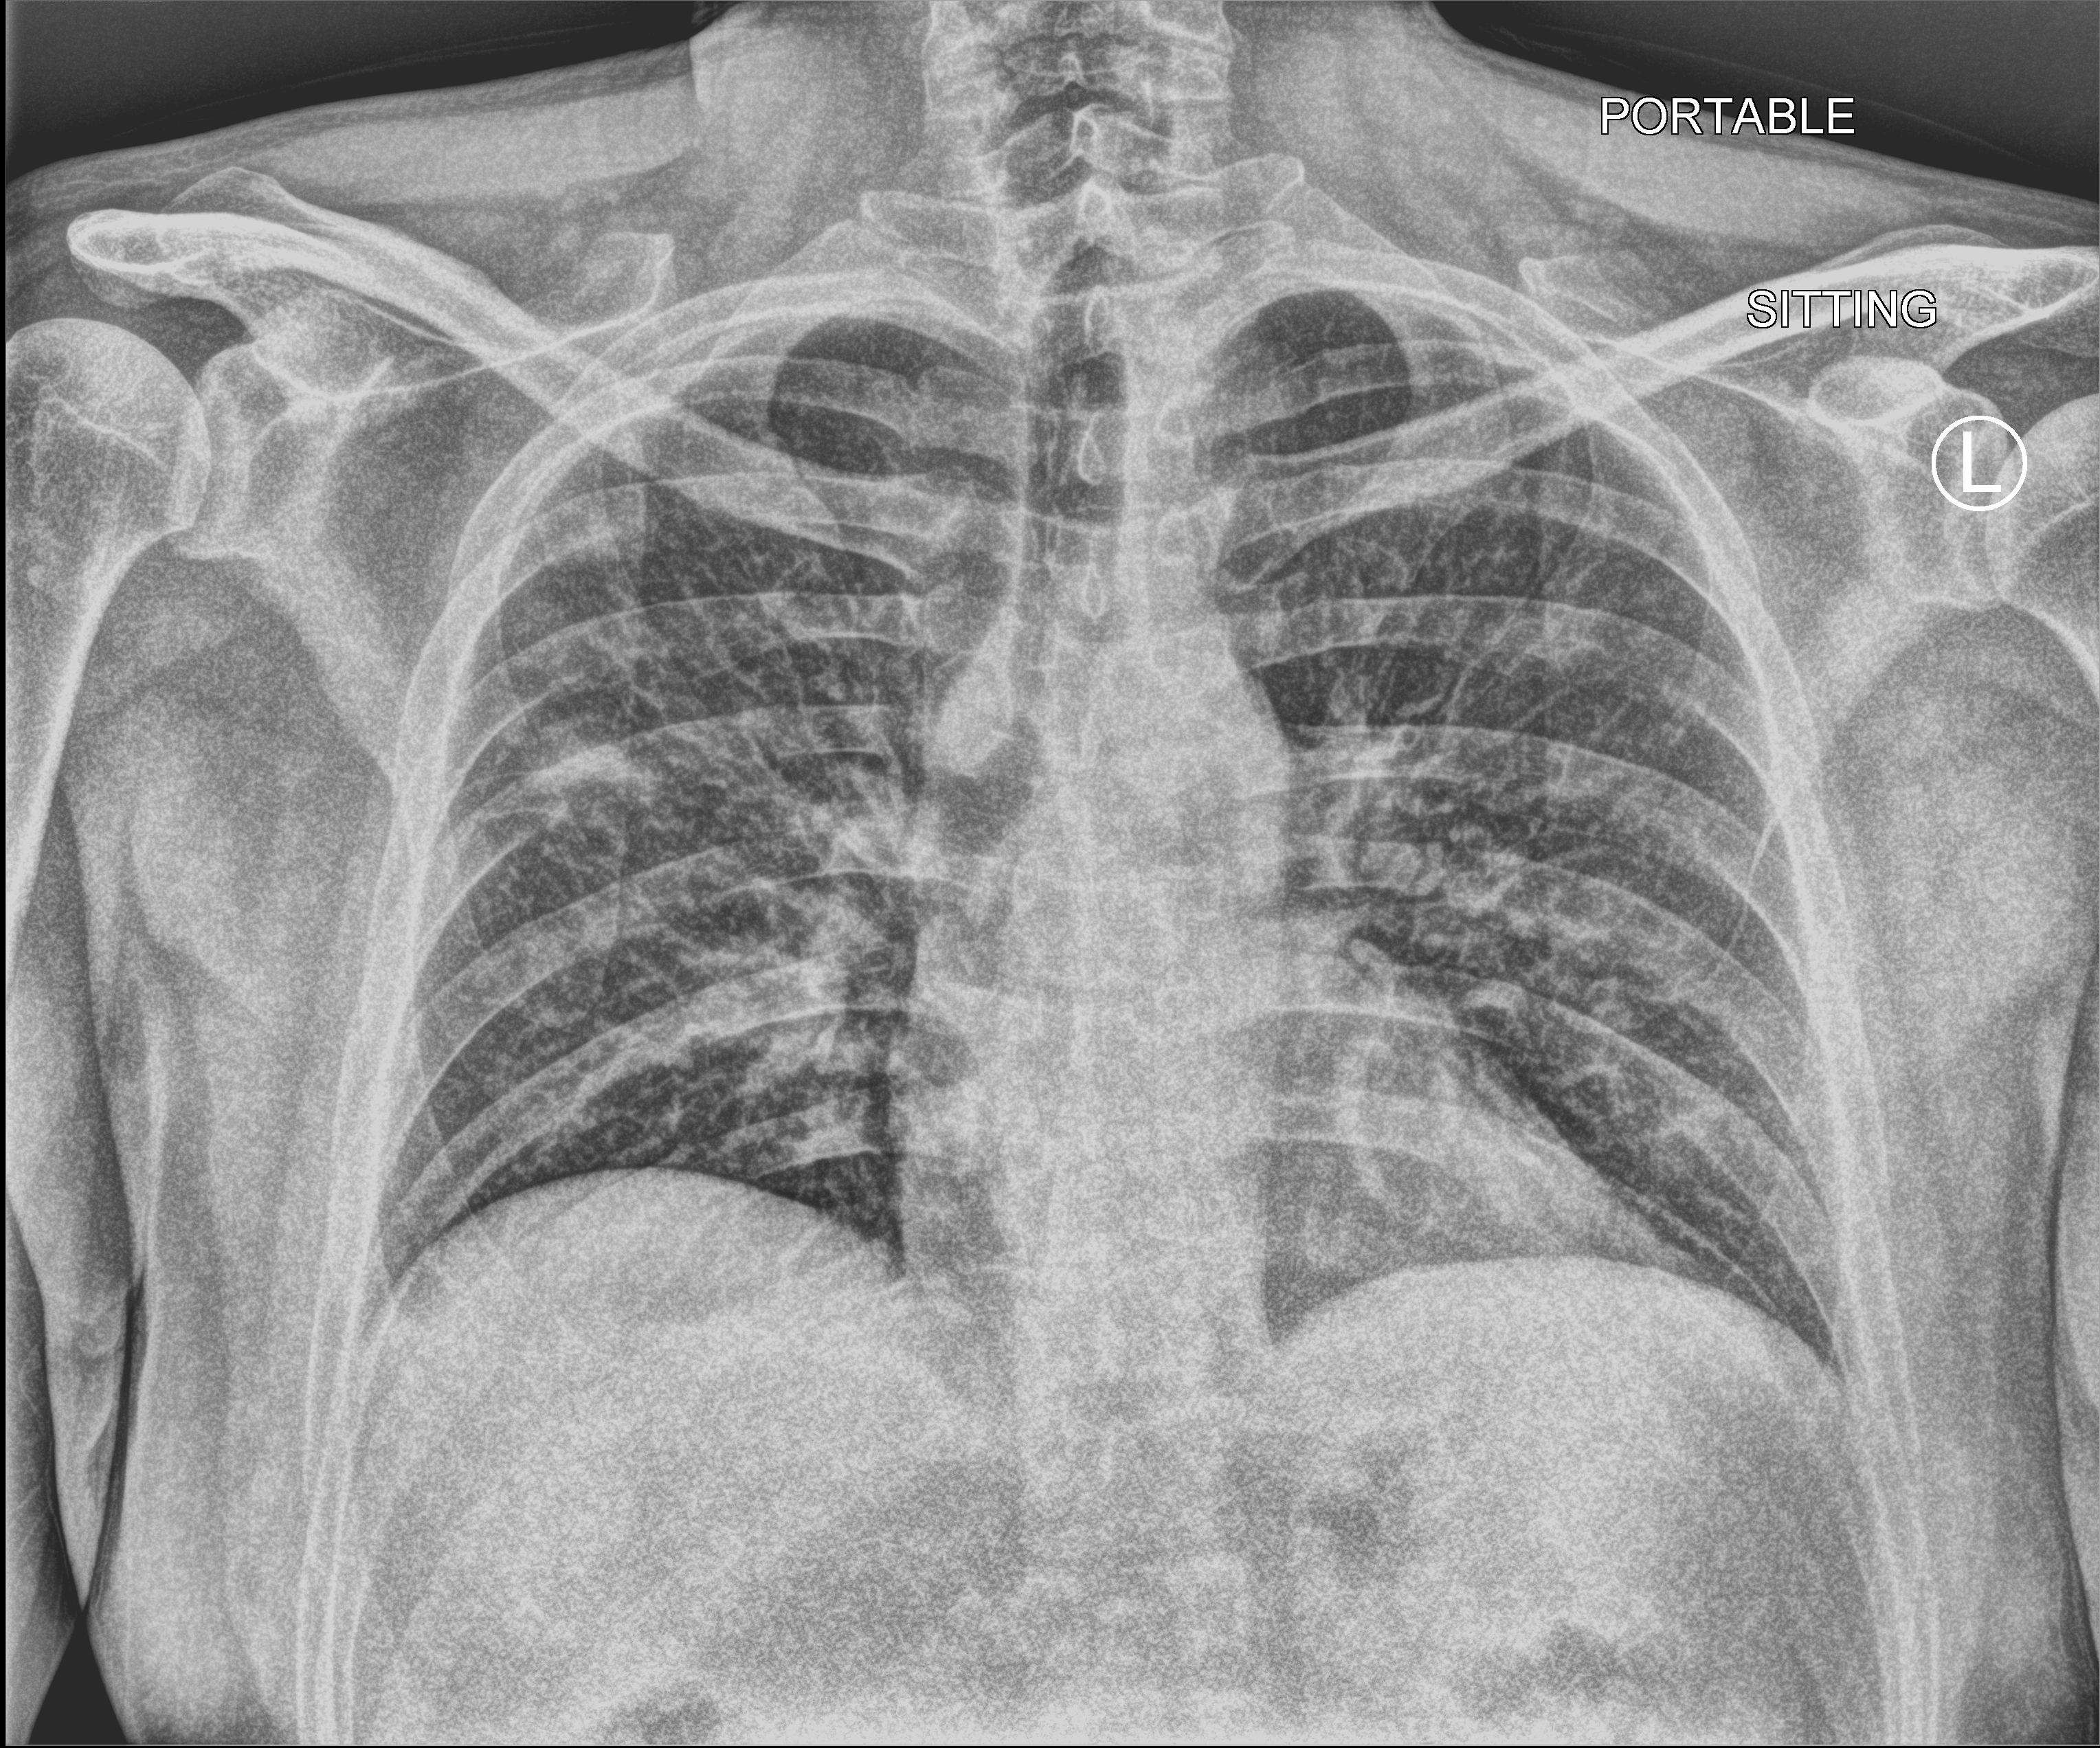
Chest X-ray (portable); anteroposterior (AP) projection. Patient hospitalised with COVID-19; male, aged 18–59 years.
From the hospital-stay record, not from the radiograph (when in the stay this image was taken is not recorded):
- admitted to intensive care during this hospital stay: no